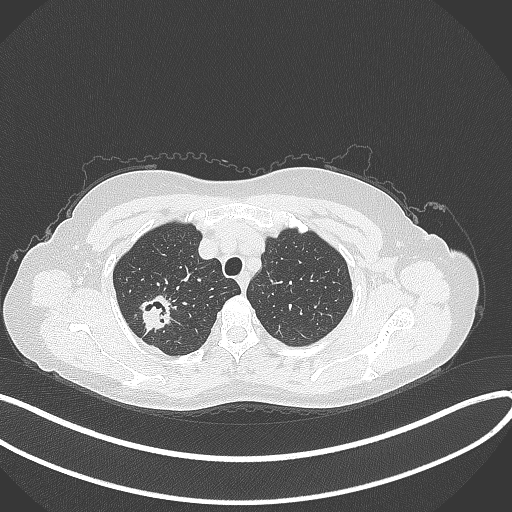
Chest CT, one axial slice; position 300 of 337 along the scan axis; reconstruction kernel B70f; 120 kVp; lung window (W 1500 / L -600 HU); 1 mm slice thickness; 512 × 512 image matrix, field of view 400 × 400 mm. Female patient, age 50 years. From the clinical record (not read from this slice): clinical TNM (as recorded): T1c N0 M0.
Outlined on this slice (bounding box drawn by a radiologist):
- lung tumour (recorded histology: adenocarcinoma): bounding box <133,295,180,336> (left, top, right, bottom; pixels)